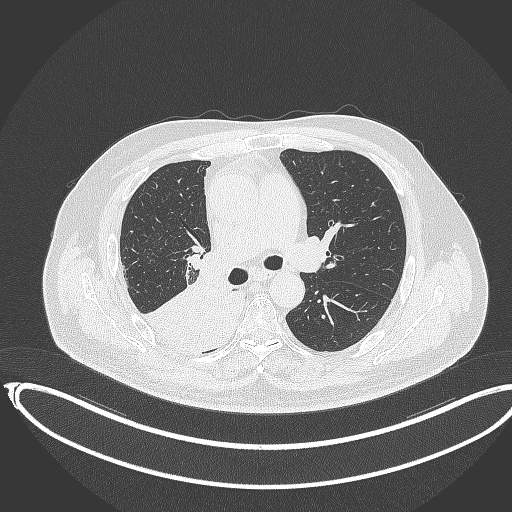
Chest CT, one axial slice; slice 216 of 403 in the series (ordered by position); 120 kVp; lung window (W 1500 / L -600 HU); 1 mm slice thickness; 512 × 512 image matrix, field of view 436 × 436 mm. Male patient, age 68 years. Case-level facts recorded for this patient, not image findings: clinical TNM (as recorded): T2a N0 M0.
Outlined on this slice (rectangle marked by the reading radiologist):
- lung tumour (recorded histology: adenocarcinoma): bounding box [x1, y1, x2, y2] px = [141, 272, 246, 360]